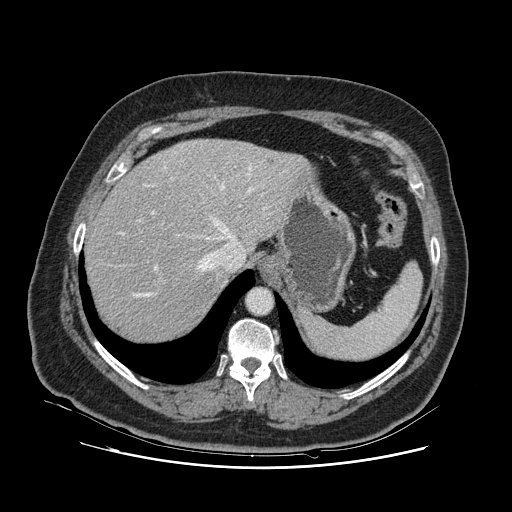
Contrast-enhanced abdominal CT, one axial slice. Slice 94 of 132 in the series (ordered by position). 120 kVp. Intravenous contrast given. Soft-tissue window (W 400 / L 40 HU). 2.5 mm slice thickness. 512 × 512 image matrix, field of view 391 × 391 mm. Female patient, age 73 years. Case-level facts recorded for this patient, not image findings: diagnosis: colorectal cancer liver metastases, imaged before liver resection; multiple liver metastases: no; largest metastasis: 7 cm.
Outlined on this slice (manually delineated by an expert):
- hepatic veins: box from (x=114, y=166) to (x=255, y=298) px
- liver: (x=86, y=140)–(x=304, y=341)
- planned liver remnant (the part of the liver to remain after resection): (x=86, y=160)–(x=234, y=342)
- portal vein (with intrahepatic branches): (x=152, y=211)–(x=158, y=271)